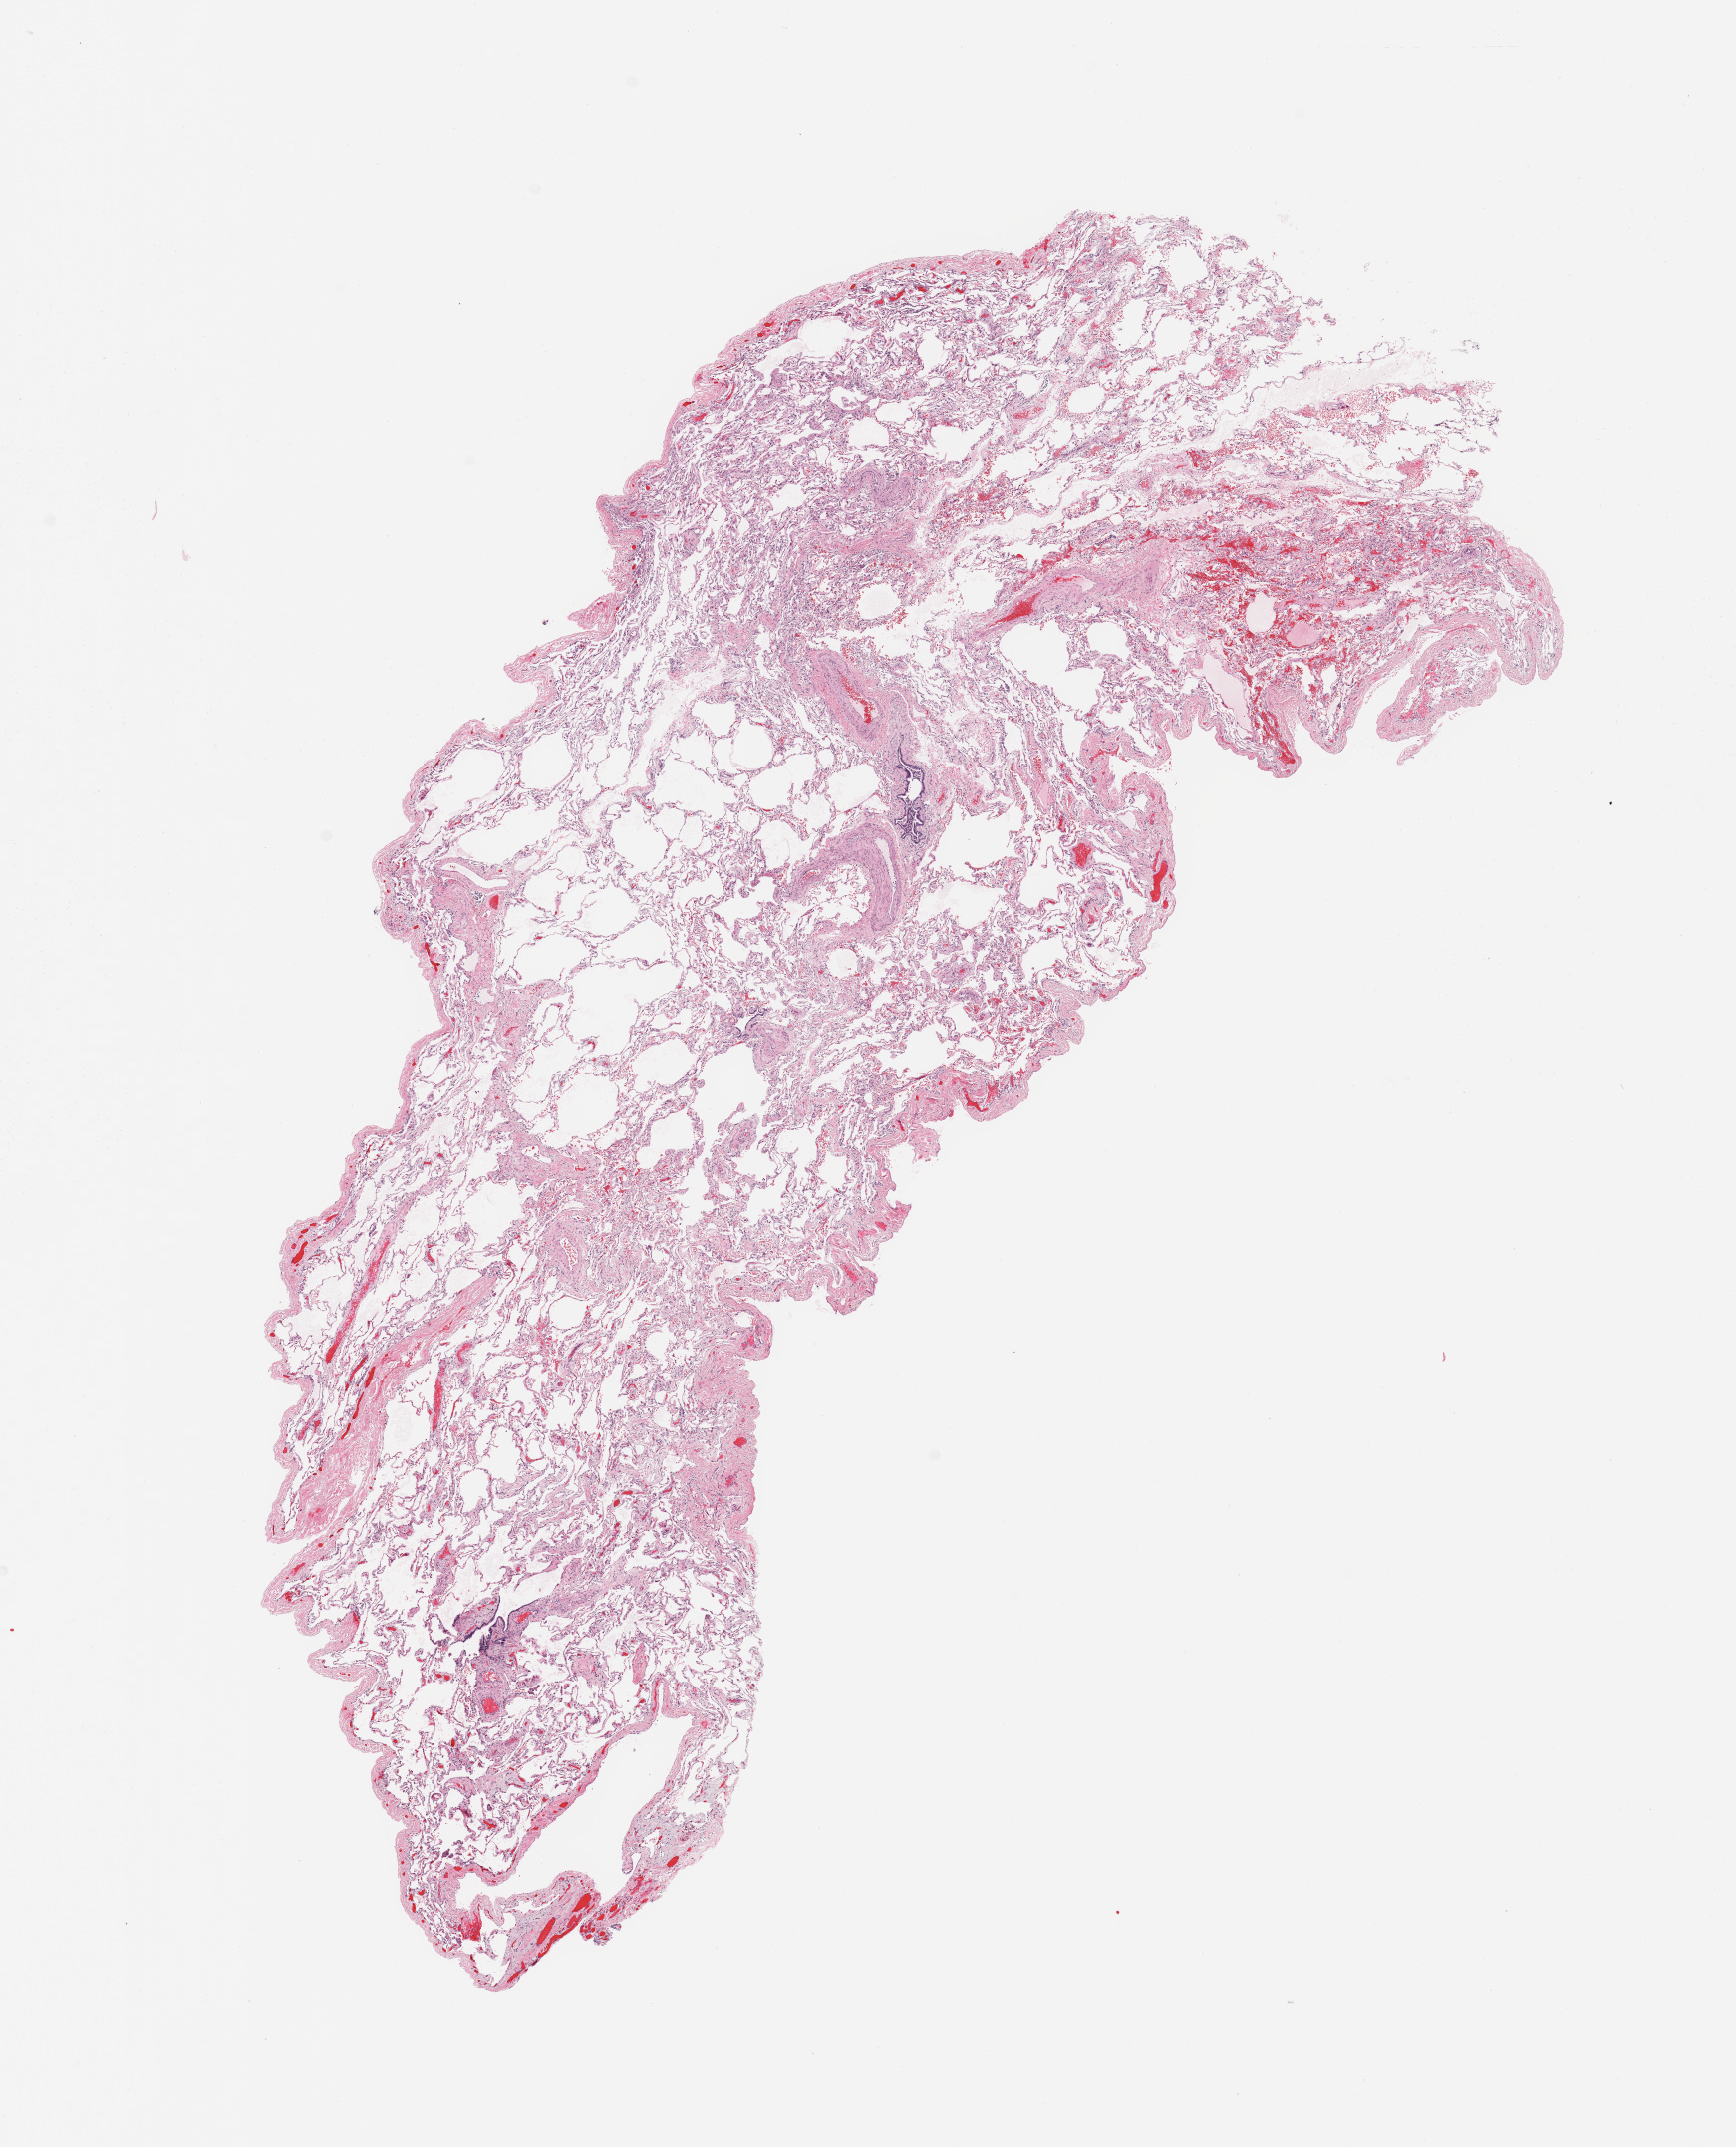
H&E whole-slide image, low-resolution overview of the scanned area, about 13.8 x 17.0 mm, normal (non-tumour) tissue sample, sampled site: lung. Patient: female, age 66 years.
* this section: normal (non-tumour) tissue from the same patient
* patient diagnosis: Adenocarcinoma, NOS